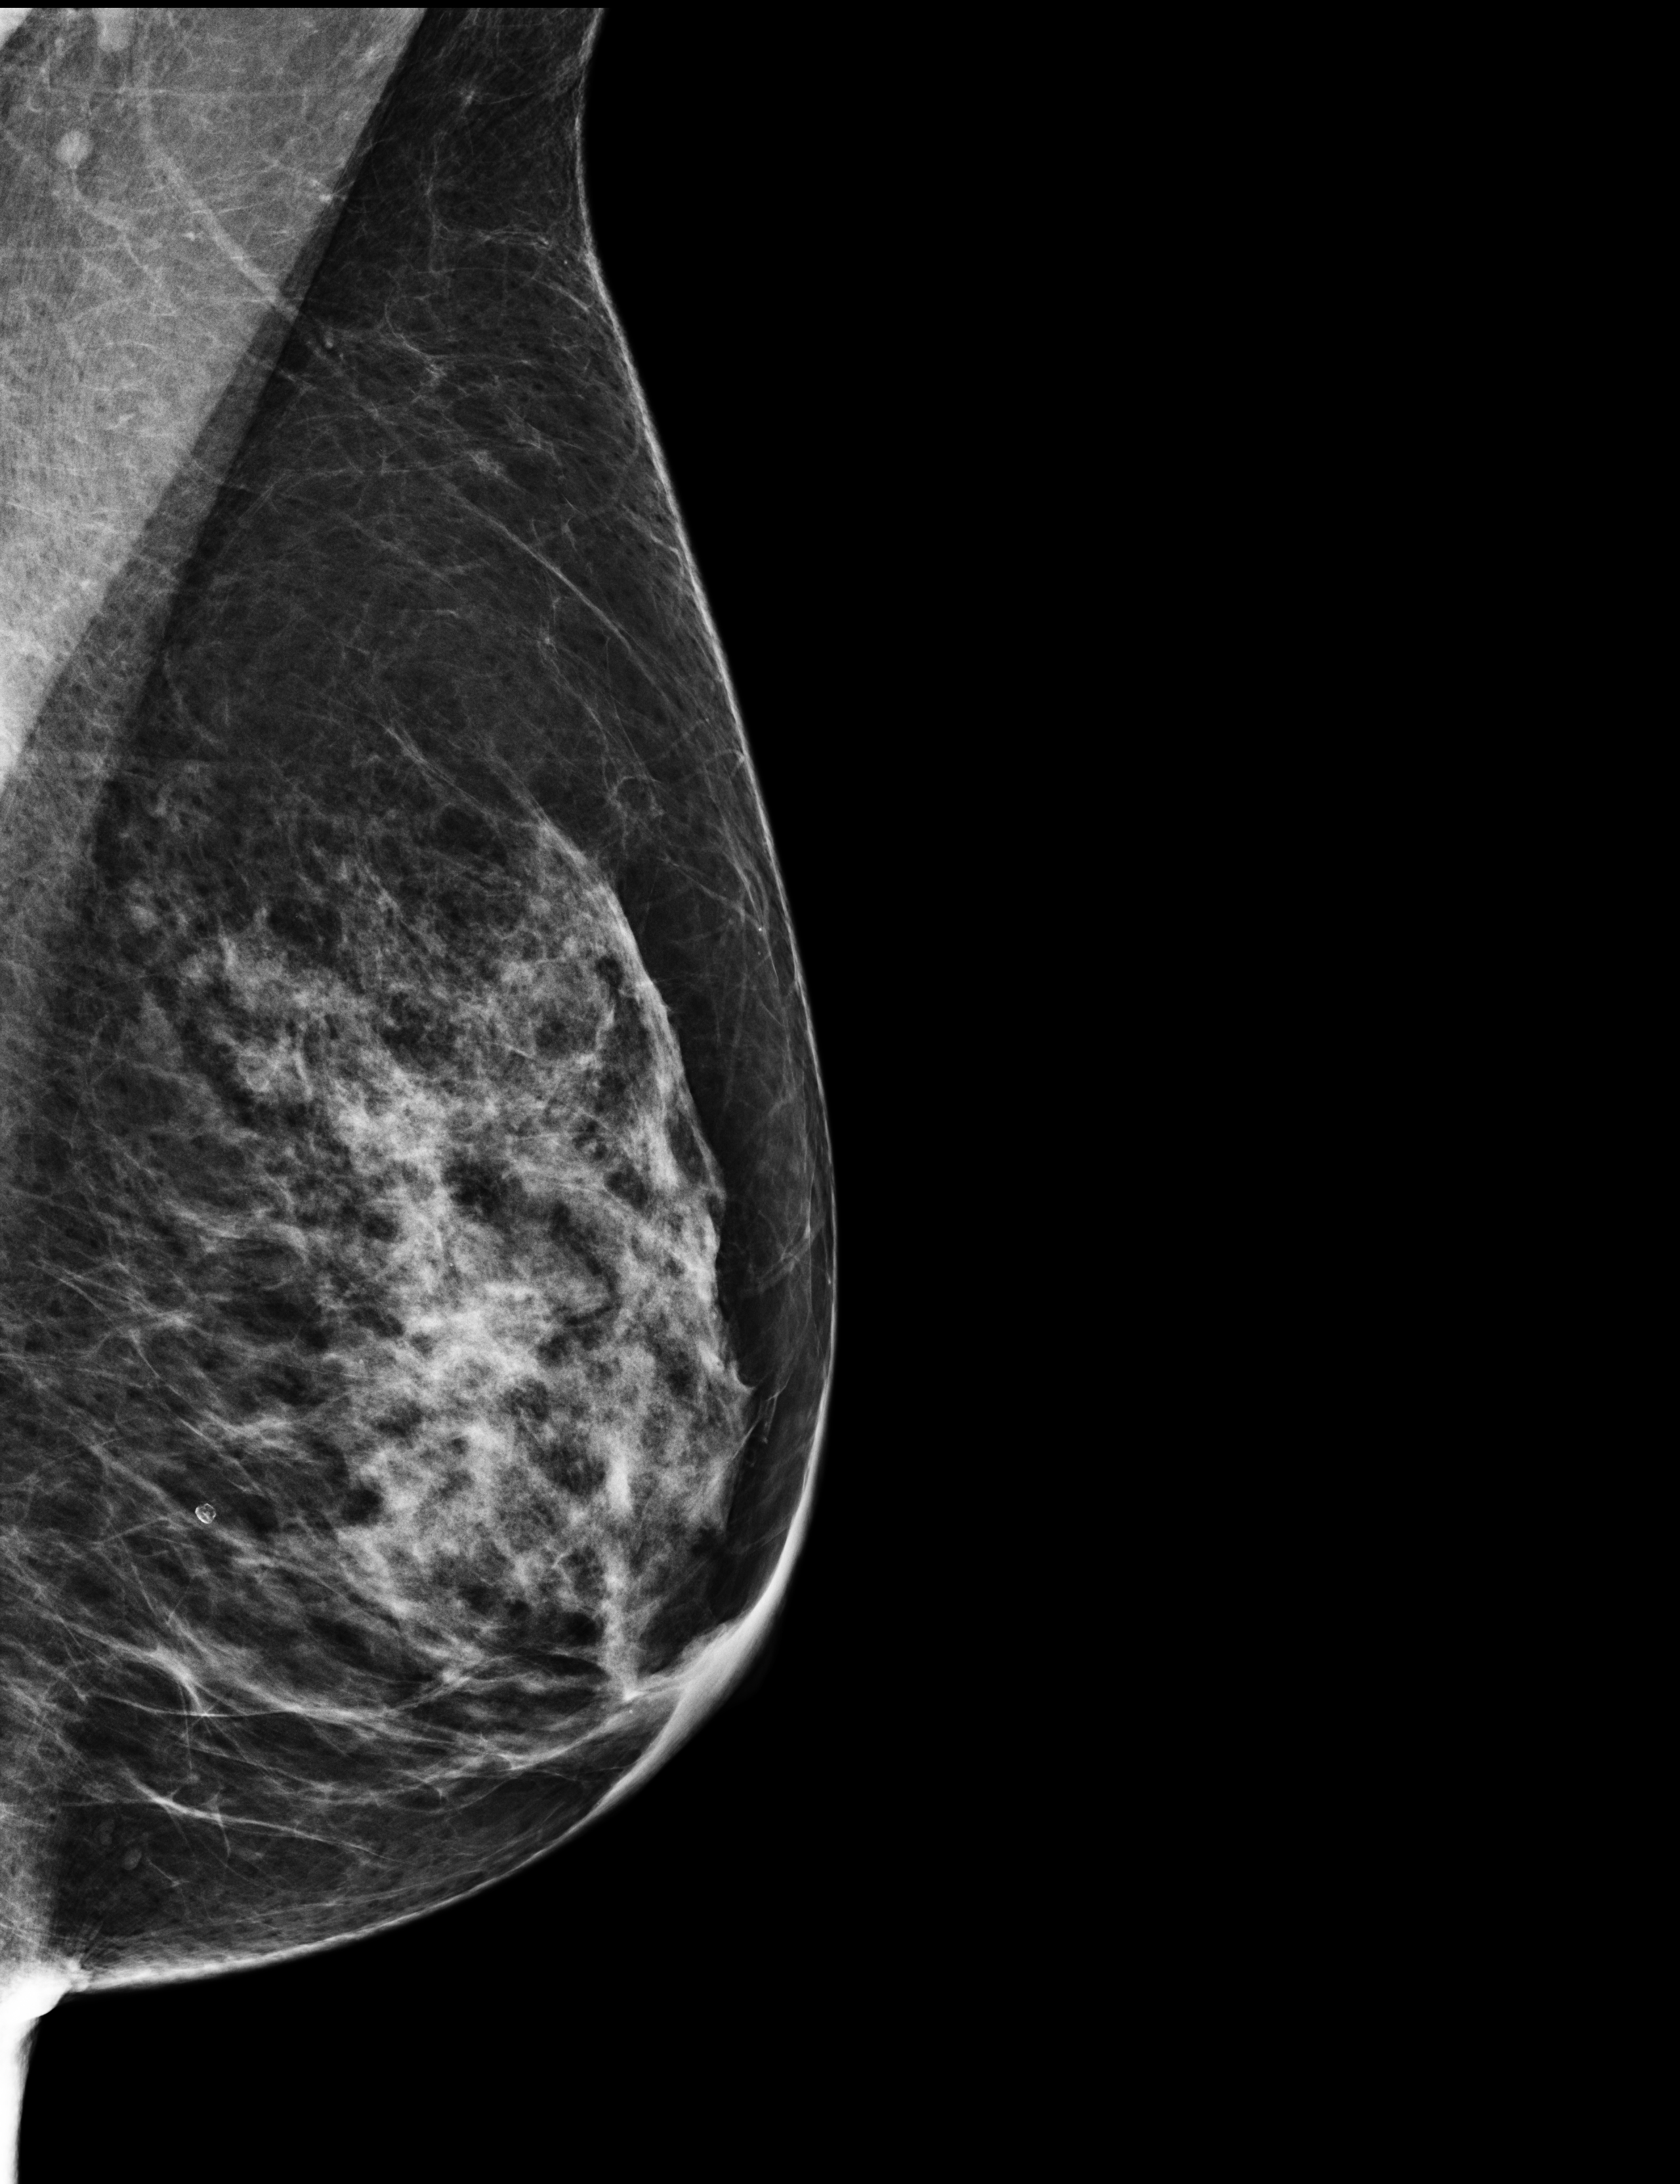
Screening examination; compressed breast thickness 56 mm.
Image type: full-field digital mammogram. Breast: left. Projection: medio-lateral oblique projection.